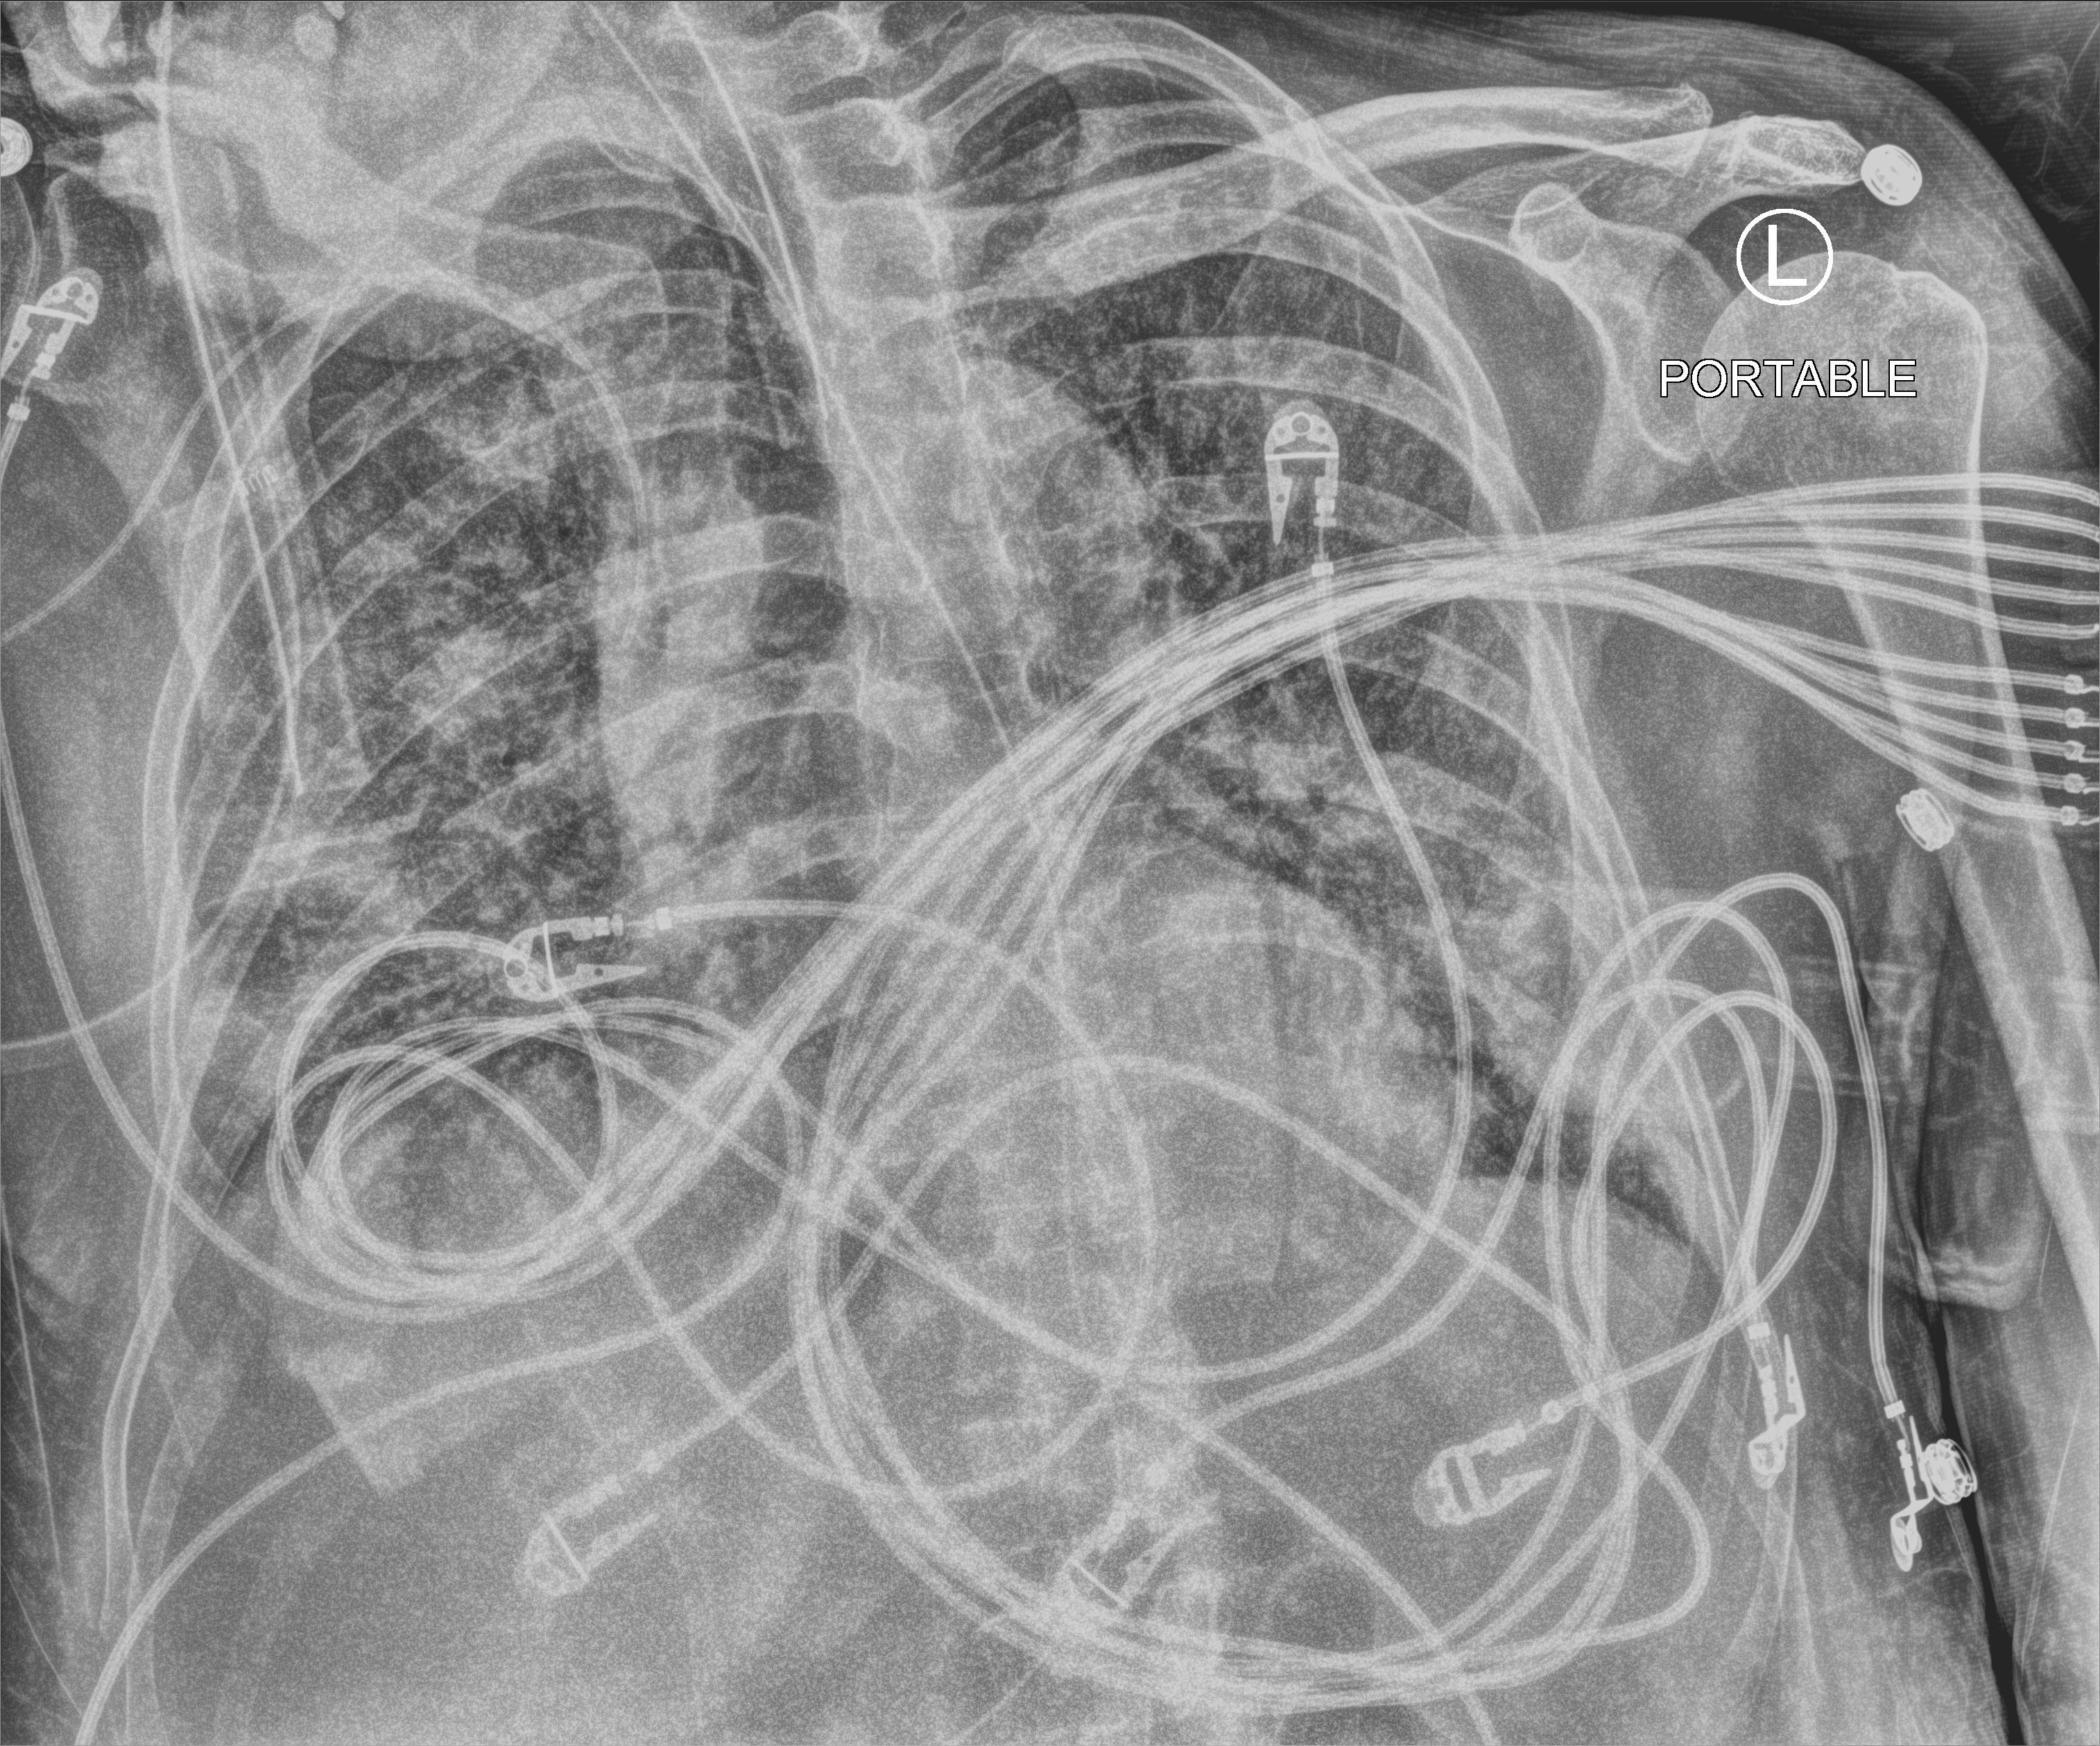
Portable chest radiograph, anteroposterior (AP) projection. Male patient hospitalised with COVID-19, age 60–74 years.
Hospital-stay facts (about this admission, not read from this image; timing relative to this image not recorded):
- COPD (admission record): no
- diabetes (admission record): no